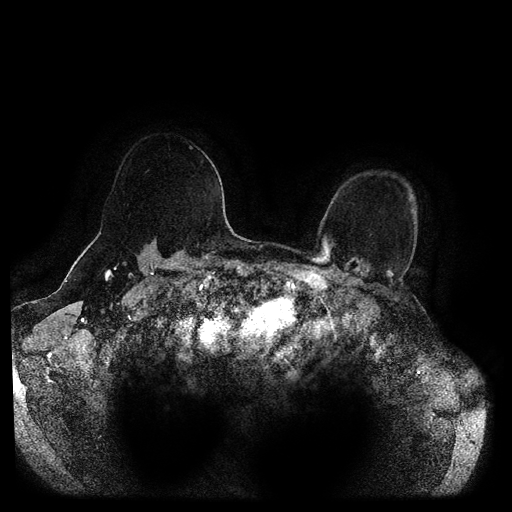
Breast MRI (dynamic contrast-enhanced, multi-phase), one axial slice. Position 82 of 116 along the scan axis. Dynamic contrast-enhanced series, time point 2 of 5 at this slice position (early post-contrast). 1.5 T. TE 2.6 ms, TR 5.3 ms. 512 × 512 image matrix, field of view 370 × 370 mm. Patient: female, 55 years.
Outlined on this slice (semi-automatic segmentation, software-assisted and operator-edited):
- breast lesion (labelled benign in the annotation): bounding box (x1, y1, x2, y2) in pixels: (343, 256, 394, 289)